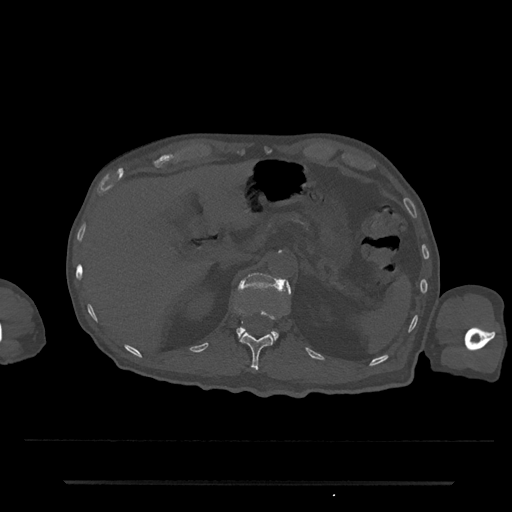
CT including the spine, one axial slice; slice 173 of 797 in the series (ordered by position); reconstruction kernel Br40s/3; bone window (W 1800 / L 400 HU); 0.5 mm slice thickness; 512 × 512 image matrix. Male patient, age 74 years. Case-level facts recorded for this patient, not image findings: primary cancer: prostate.
Structures marked on this image (semi-automatic segmentation, software-assisted and operator-edited):
- L1 vertebra: bounding box [x1, y1, x2, y2] px = [235, 272, 291, 340]
- T12 vertebra: [240, 310, 275, 371]